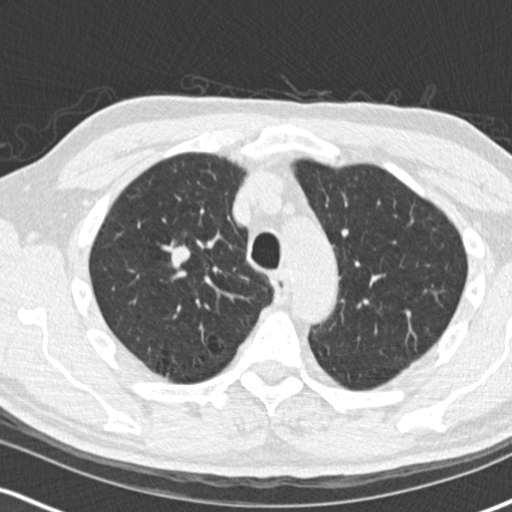
Low-dose screening chest CT, one axial slice; slice 117 of 170 in the series (ordered by position); lung window (W 1500 / L -600 HU); 2 mm slice thickness; 512 × 512 image matrix, field of view 320 × 320 mm.
Outlined on this slice (outlined manually by an expert reader):
- lesion 1 (tumor, upper lobe of right lung): bounding box <171,246,190,268> (left, top, right, bottom; pixels)